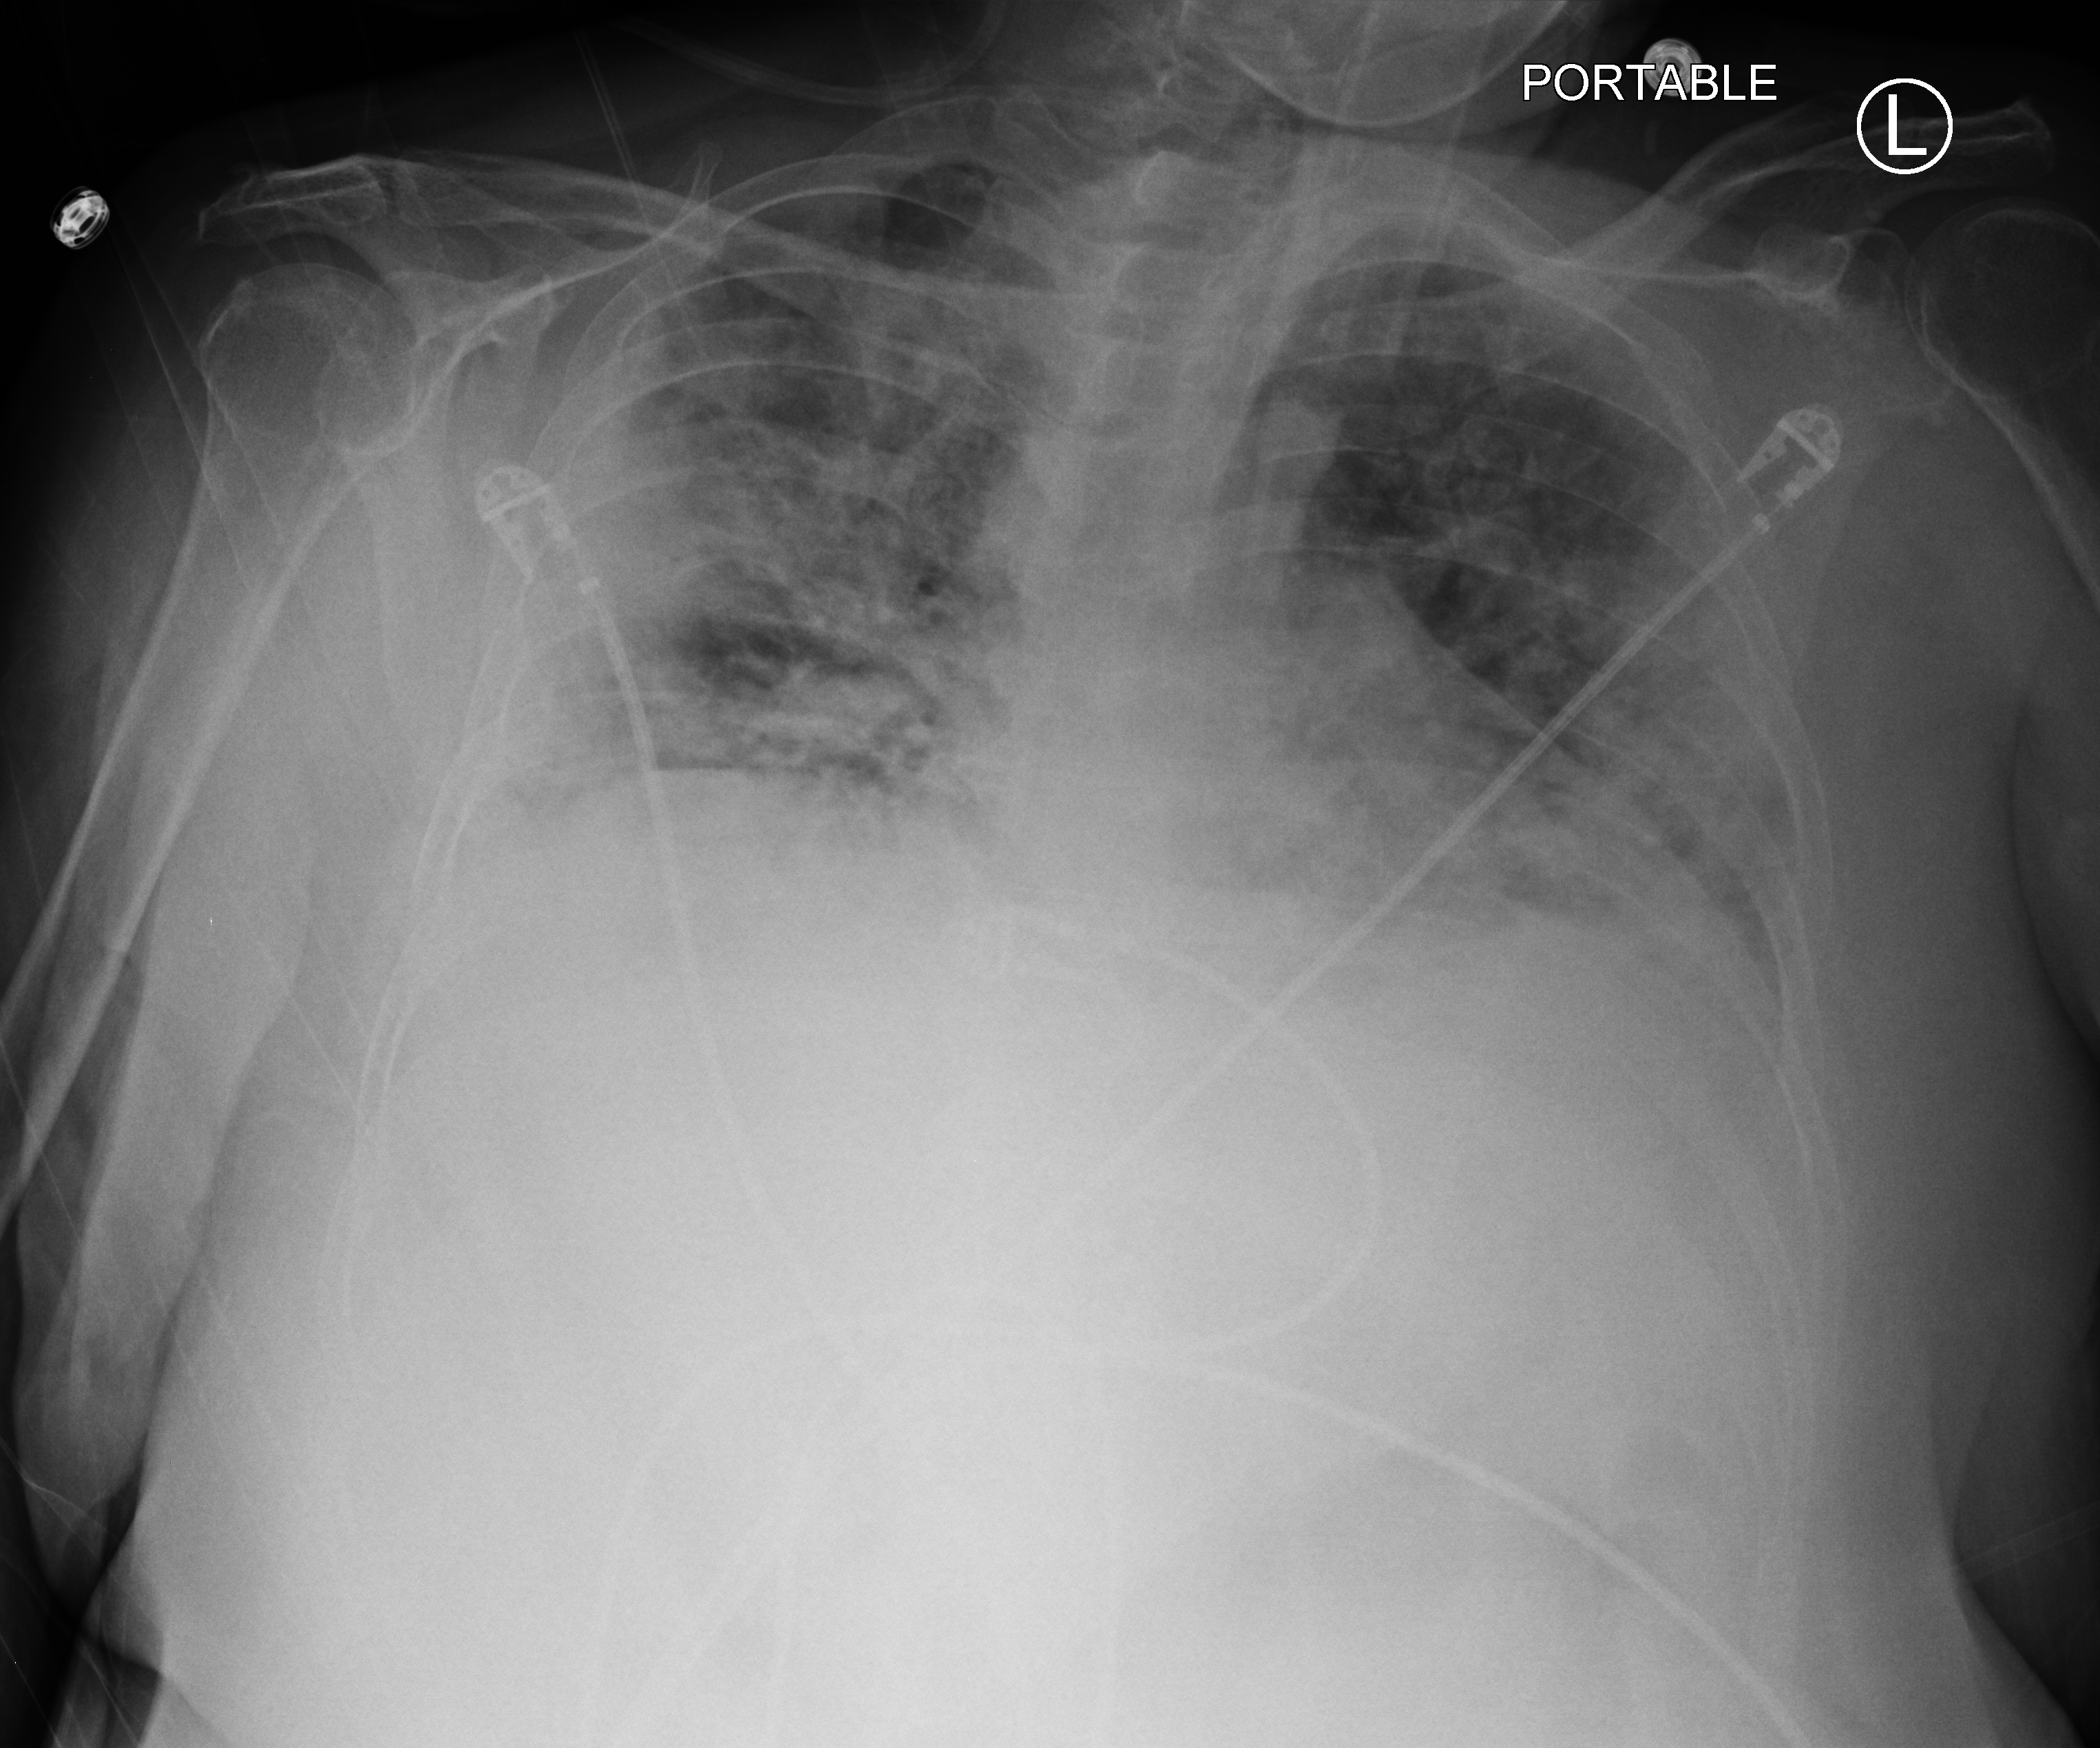
Bedside chest radiograph (computed radiography). Patient hospitalised with COVID-19; female, aged 18–59 years.
From the hospital-stay record, not from the radiograph (when in the stay this image was taken is not recorded):
- mechanically ventilated during this hospital stay: no
- COPD (admission record): no
- admitted to intensive care during this hospital stay: yes